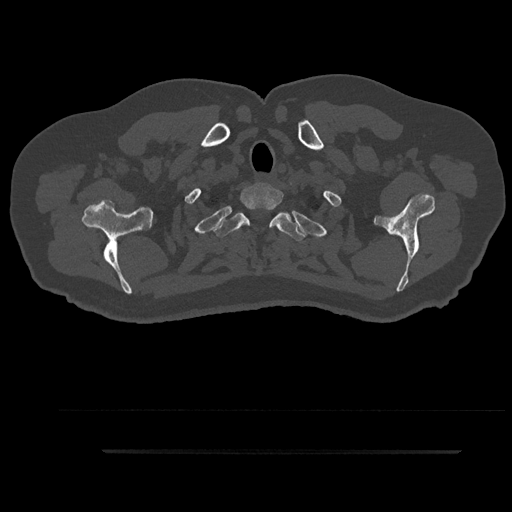
CT including the spine, one axial slice. Slice 776 of 797 in the series (ordered by position). Reconstruction kernel Br40s/3. Bone window (W 1800 / L 400 HU). 0.5 mm slice thickness. 512 × 512 image matrix. Male patient, age 63 years. Case-level facts recorded for this patient, not image findings: primary cancer: renal; vertebrae with lytic lesions (as recorded): T8.
Structures marked on this image (semi-automatic segmentation, software-assisted and operator-edited):
- T1 vertebra: bounding box (x1, y1, x2, y2) in pixels: (240, 185, 289, 216)
- T2 vertebra: (213, 207, 306, 240)